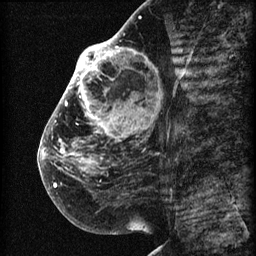
Breast MRI (dynamic contrast-enhanced), one sagittal slice; slice 31 of 60 in the series (ordered by position); 3 images stored at this slice position (order not interpretable as contrast timing); 1.5 T; TE 4.2 ms, TR 22.7 ms; 2 mm slice thickness; 256 × 256 image matrix. Patient: female, 48 years. Case-level facts recorded for this patient, not image findings: setting: breast cancer imaged before/during neoadjuvant chemotherapy; receptor status: triple-negative.
Annotated regions visible in this slice (semi-automatic segmentation, software-assisted and operator-edited):
- analysis volume of interest (the breast-tissue region the enhancement analysis was run in; not a lesion): box from (x=44, y=30) to (x=173, y=207) px
- tumour enhancement mask (voxels above the 90 % enhancement threshold inside the analysis volume of interest): (x=44, y=31)–(x=147, y=187)